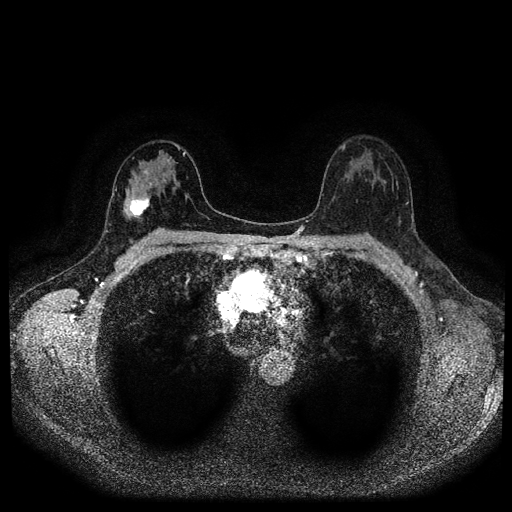
Breast MRI (dynamic contrast-enhanced, multi-phase), one axial slice. Position 62 of 116 along the scan axis. Dynamic contrast-enhanced series, time point 2 of 5 at this slice position (early post-contrast). 1.5 T. TE 2.7 ms, TR 5.4 ms. 2 mm slice thickness. 512 × 512 image matrix, field of view 330 × 330 mm. Female patient, age 42 years.
Structures marked on this image (semi-automatically segmented with operator editing):
- breast lesion (labelled 'tumour' in the annotation; benign lesions carry a separate 'benign' label): bounding box <126,195,152,220> (left, top, right, bottom; pixels)